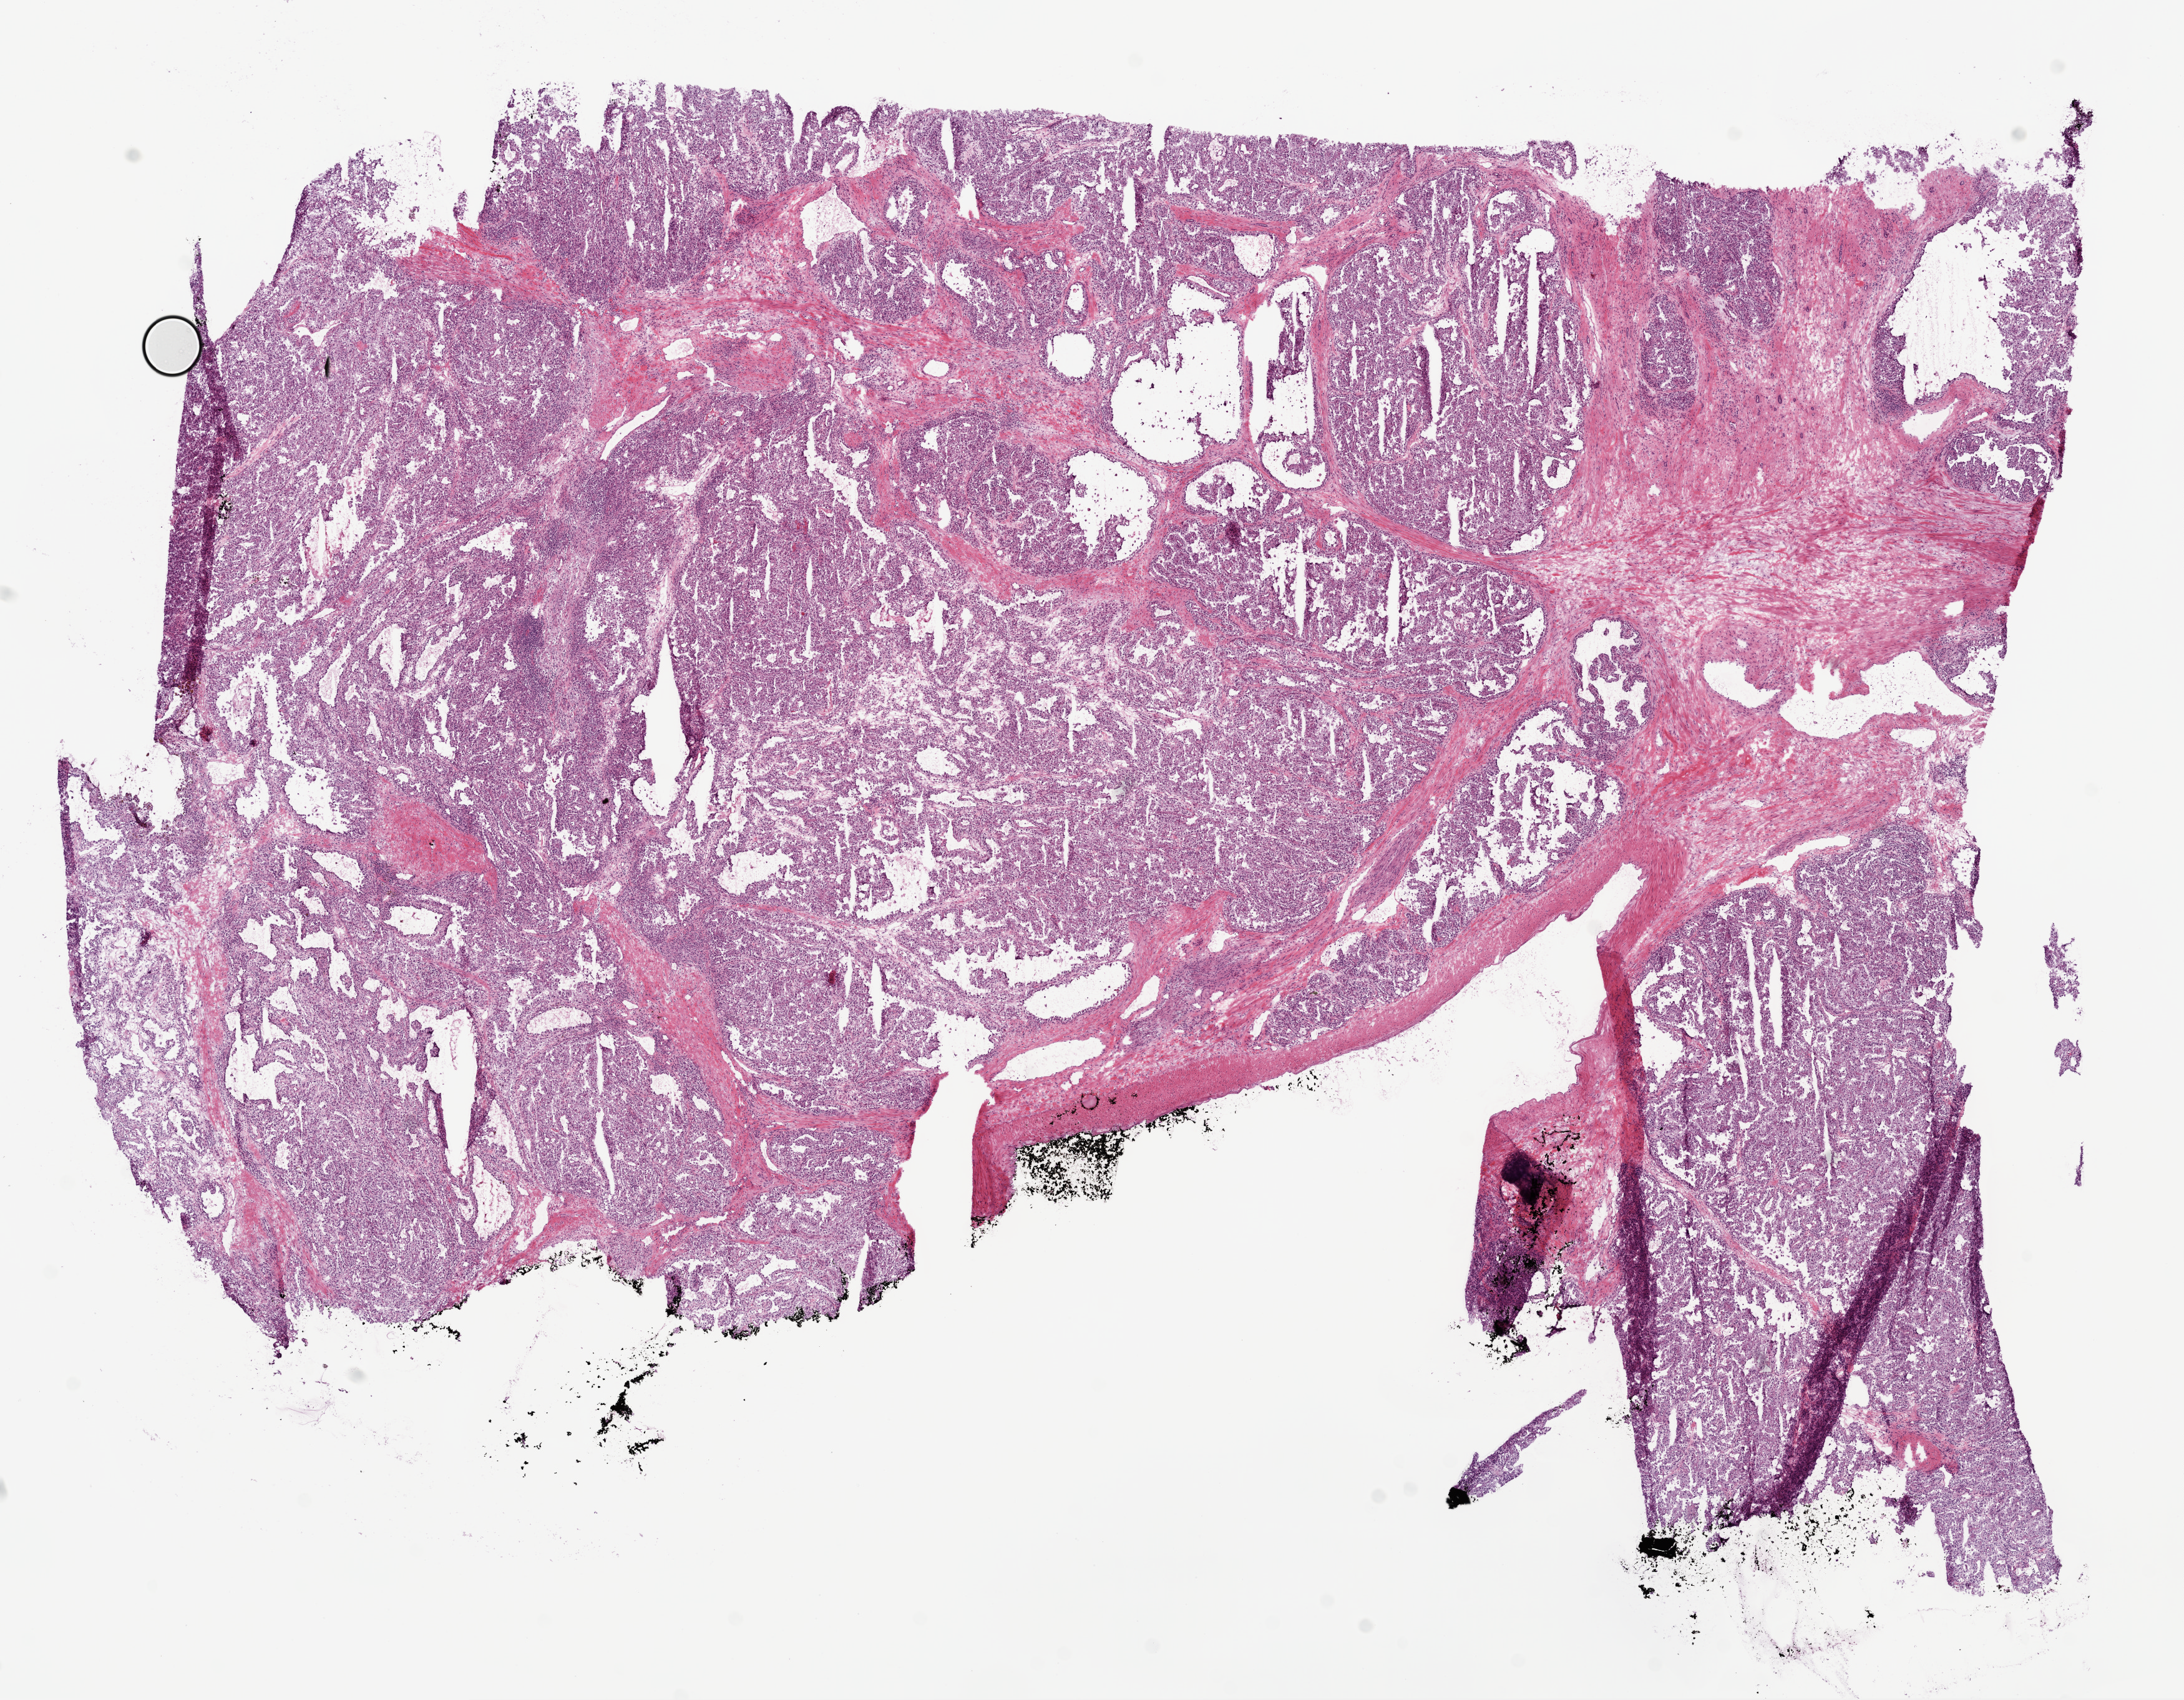
Whole-slide histology image, H&E-stained, a low-resolution overview of the entire scanned area, about 14.0 x 10.9 mm (from a 20x scan), frozen section from the bottom of the tissue portion, sample: primary tumour, kidney. Patient: male, age at initial diagnosis 67 years. Histologic grade: G2 (moderately differentiated). Composition of this section per pathologist review: tumour cells 80%, tumour nuclei 80%, normal cells 0%, stromal cells 20%, necrosis 0%.
* TNM: T2 N0 M0
* AJCC pathologic stage: II
* diagnosis: Clear cell adenocarcinoma, NOS